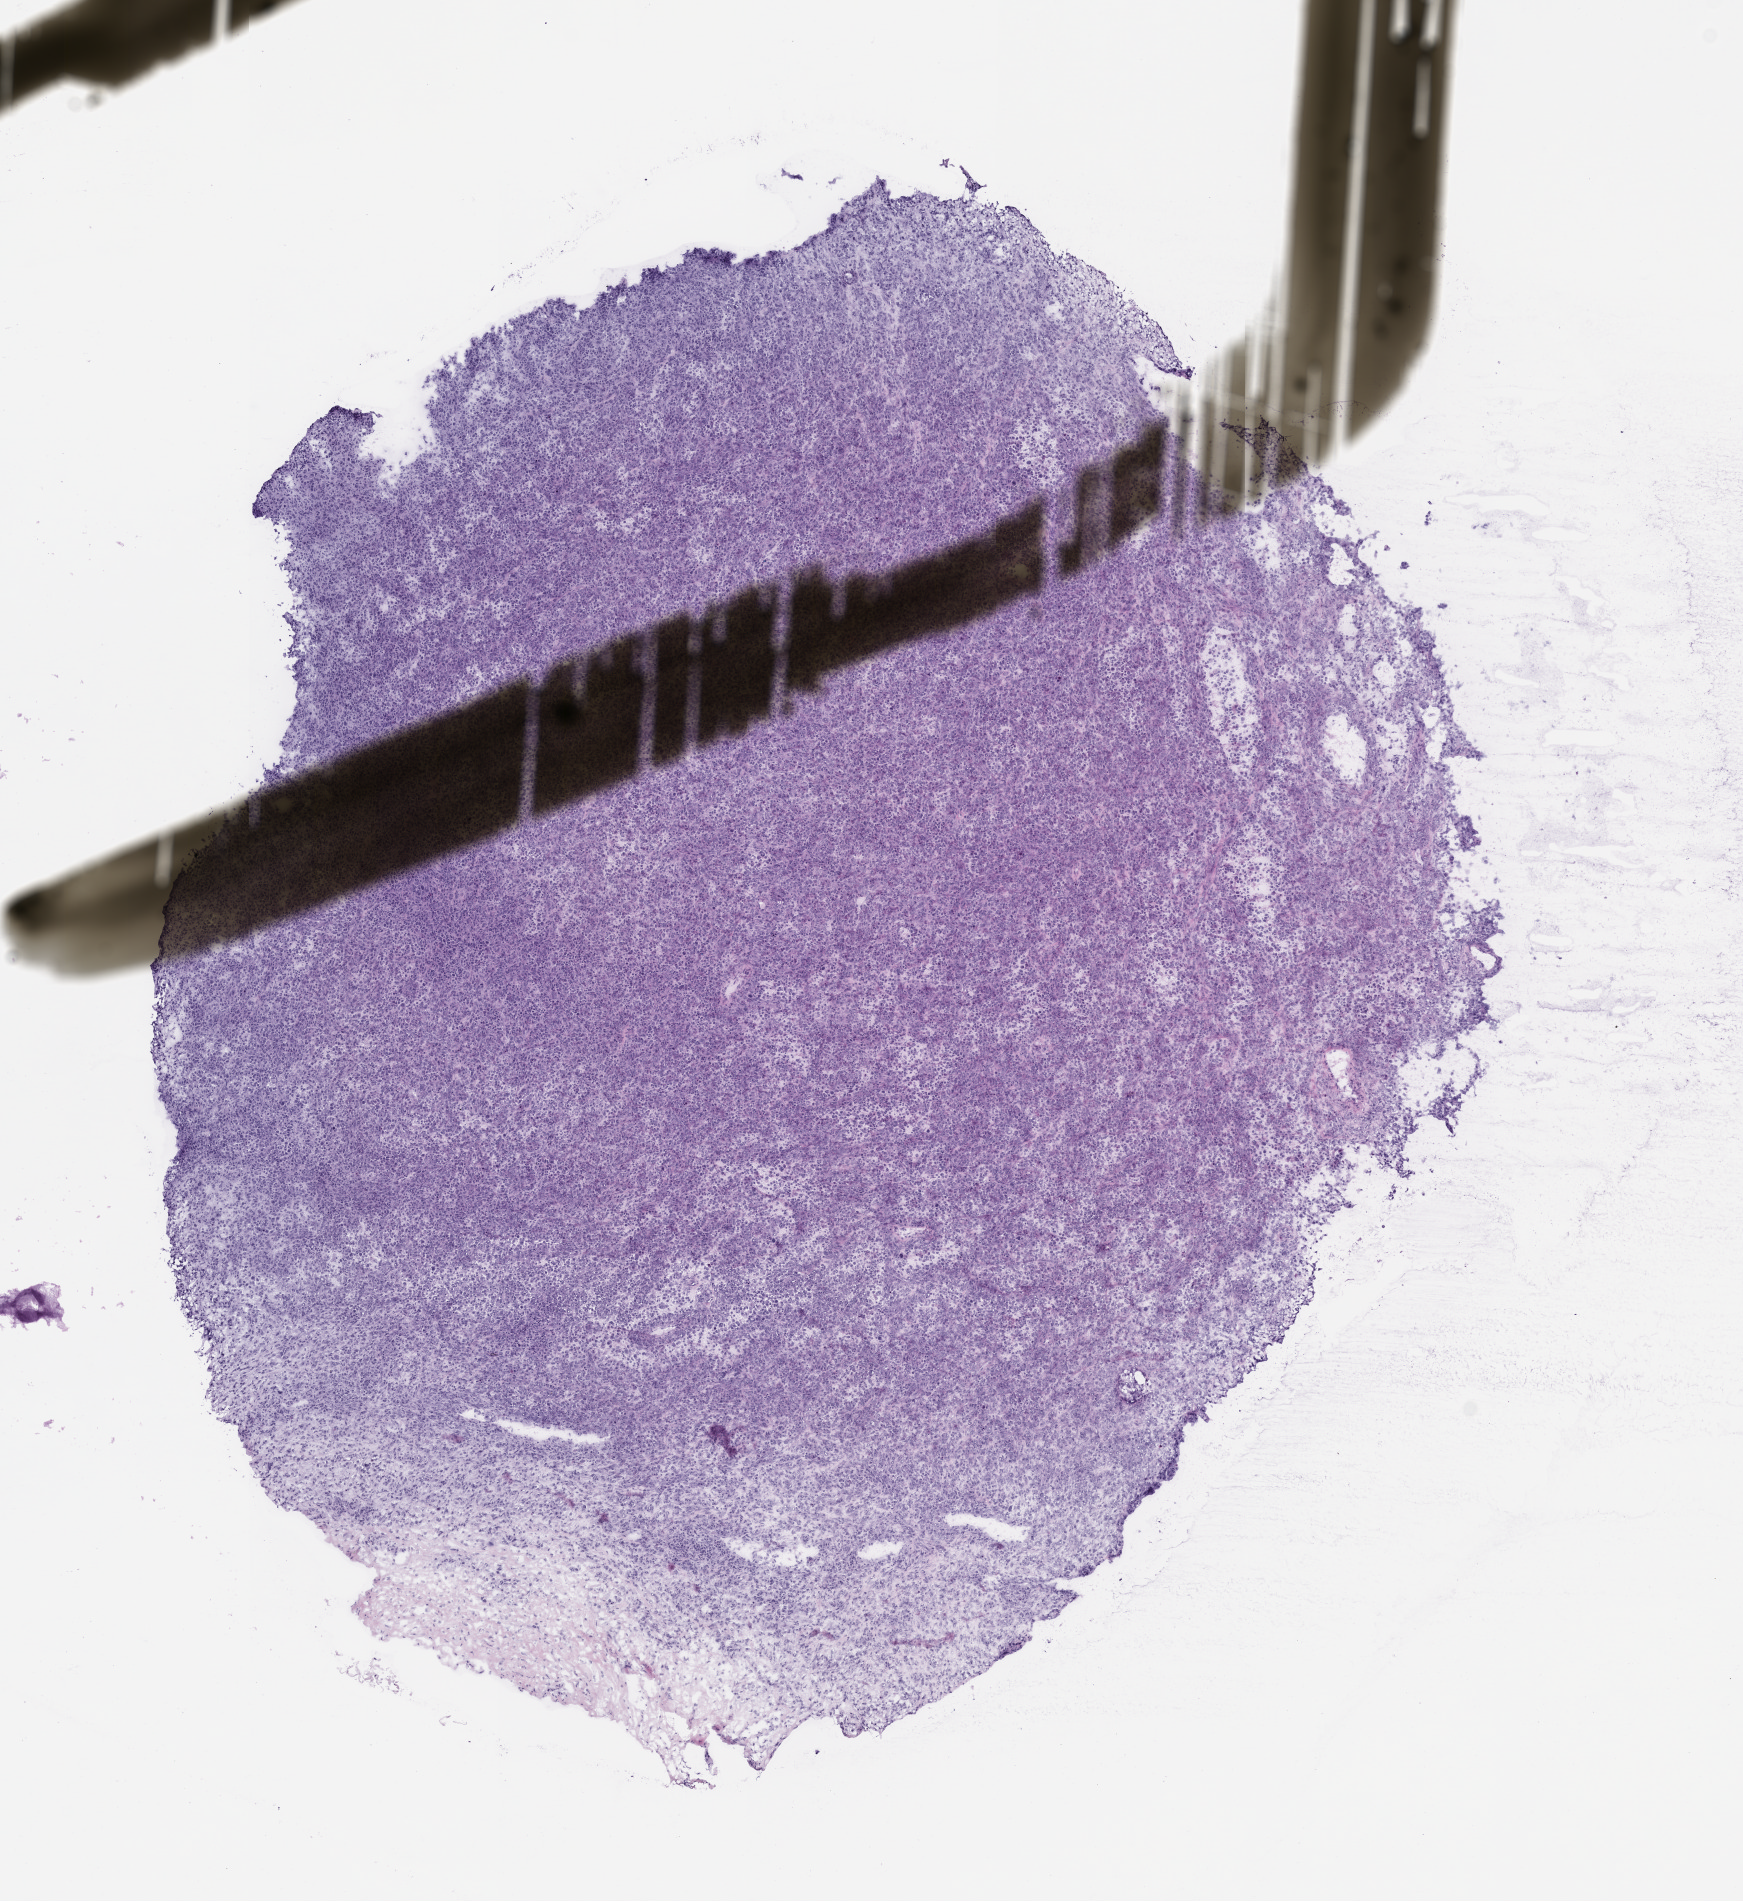
Whole-slide image, hematoxylin and eosin (H&E) stain of the patient's (originator) tumor tissue — a low-resolution overview of the entire scanned area, about 7.0 x 7.6 mm. Formalin-fixed, paraffin-embedded (FFPE) tissue. Originating tumor site category: musculoskeletal. Male patient, age 48 years.
- diagnosis: Rhabdomyosarcoma